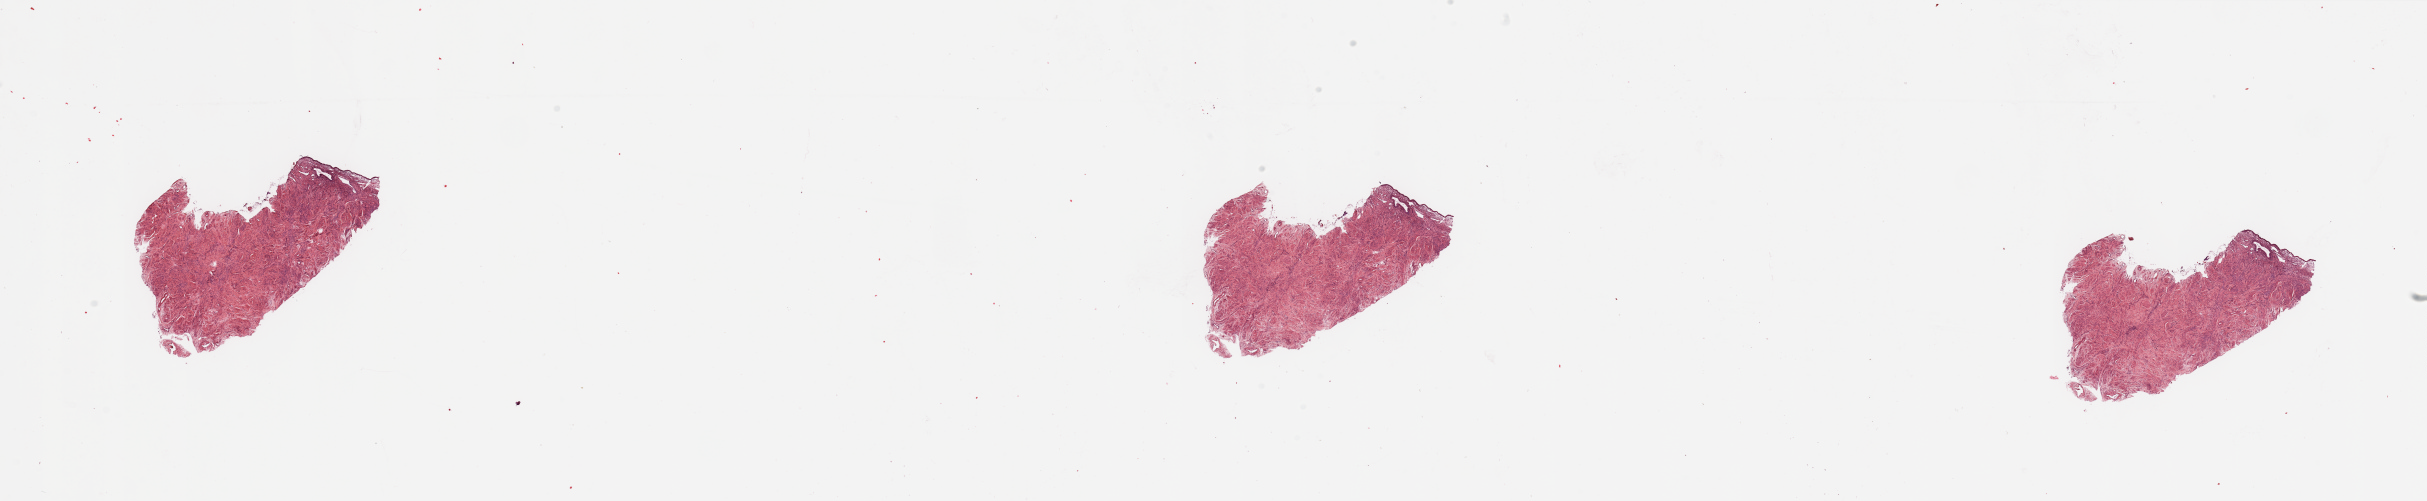
Whole-slide histology image, H&E-stained, whole scanned area (about 38.4 x 7.9 mm, from a 20x scan) shown as a low-resolution overview, normal (non-tumour) tissue sample, sampled site: uterus. Patient: female, age 63 years.
This section: normal (non-tumour) tissue from the same patient. Patient diagnosis: Endometrioid adenocarcinoma, NOS.